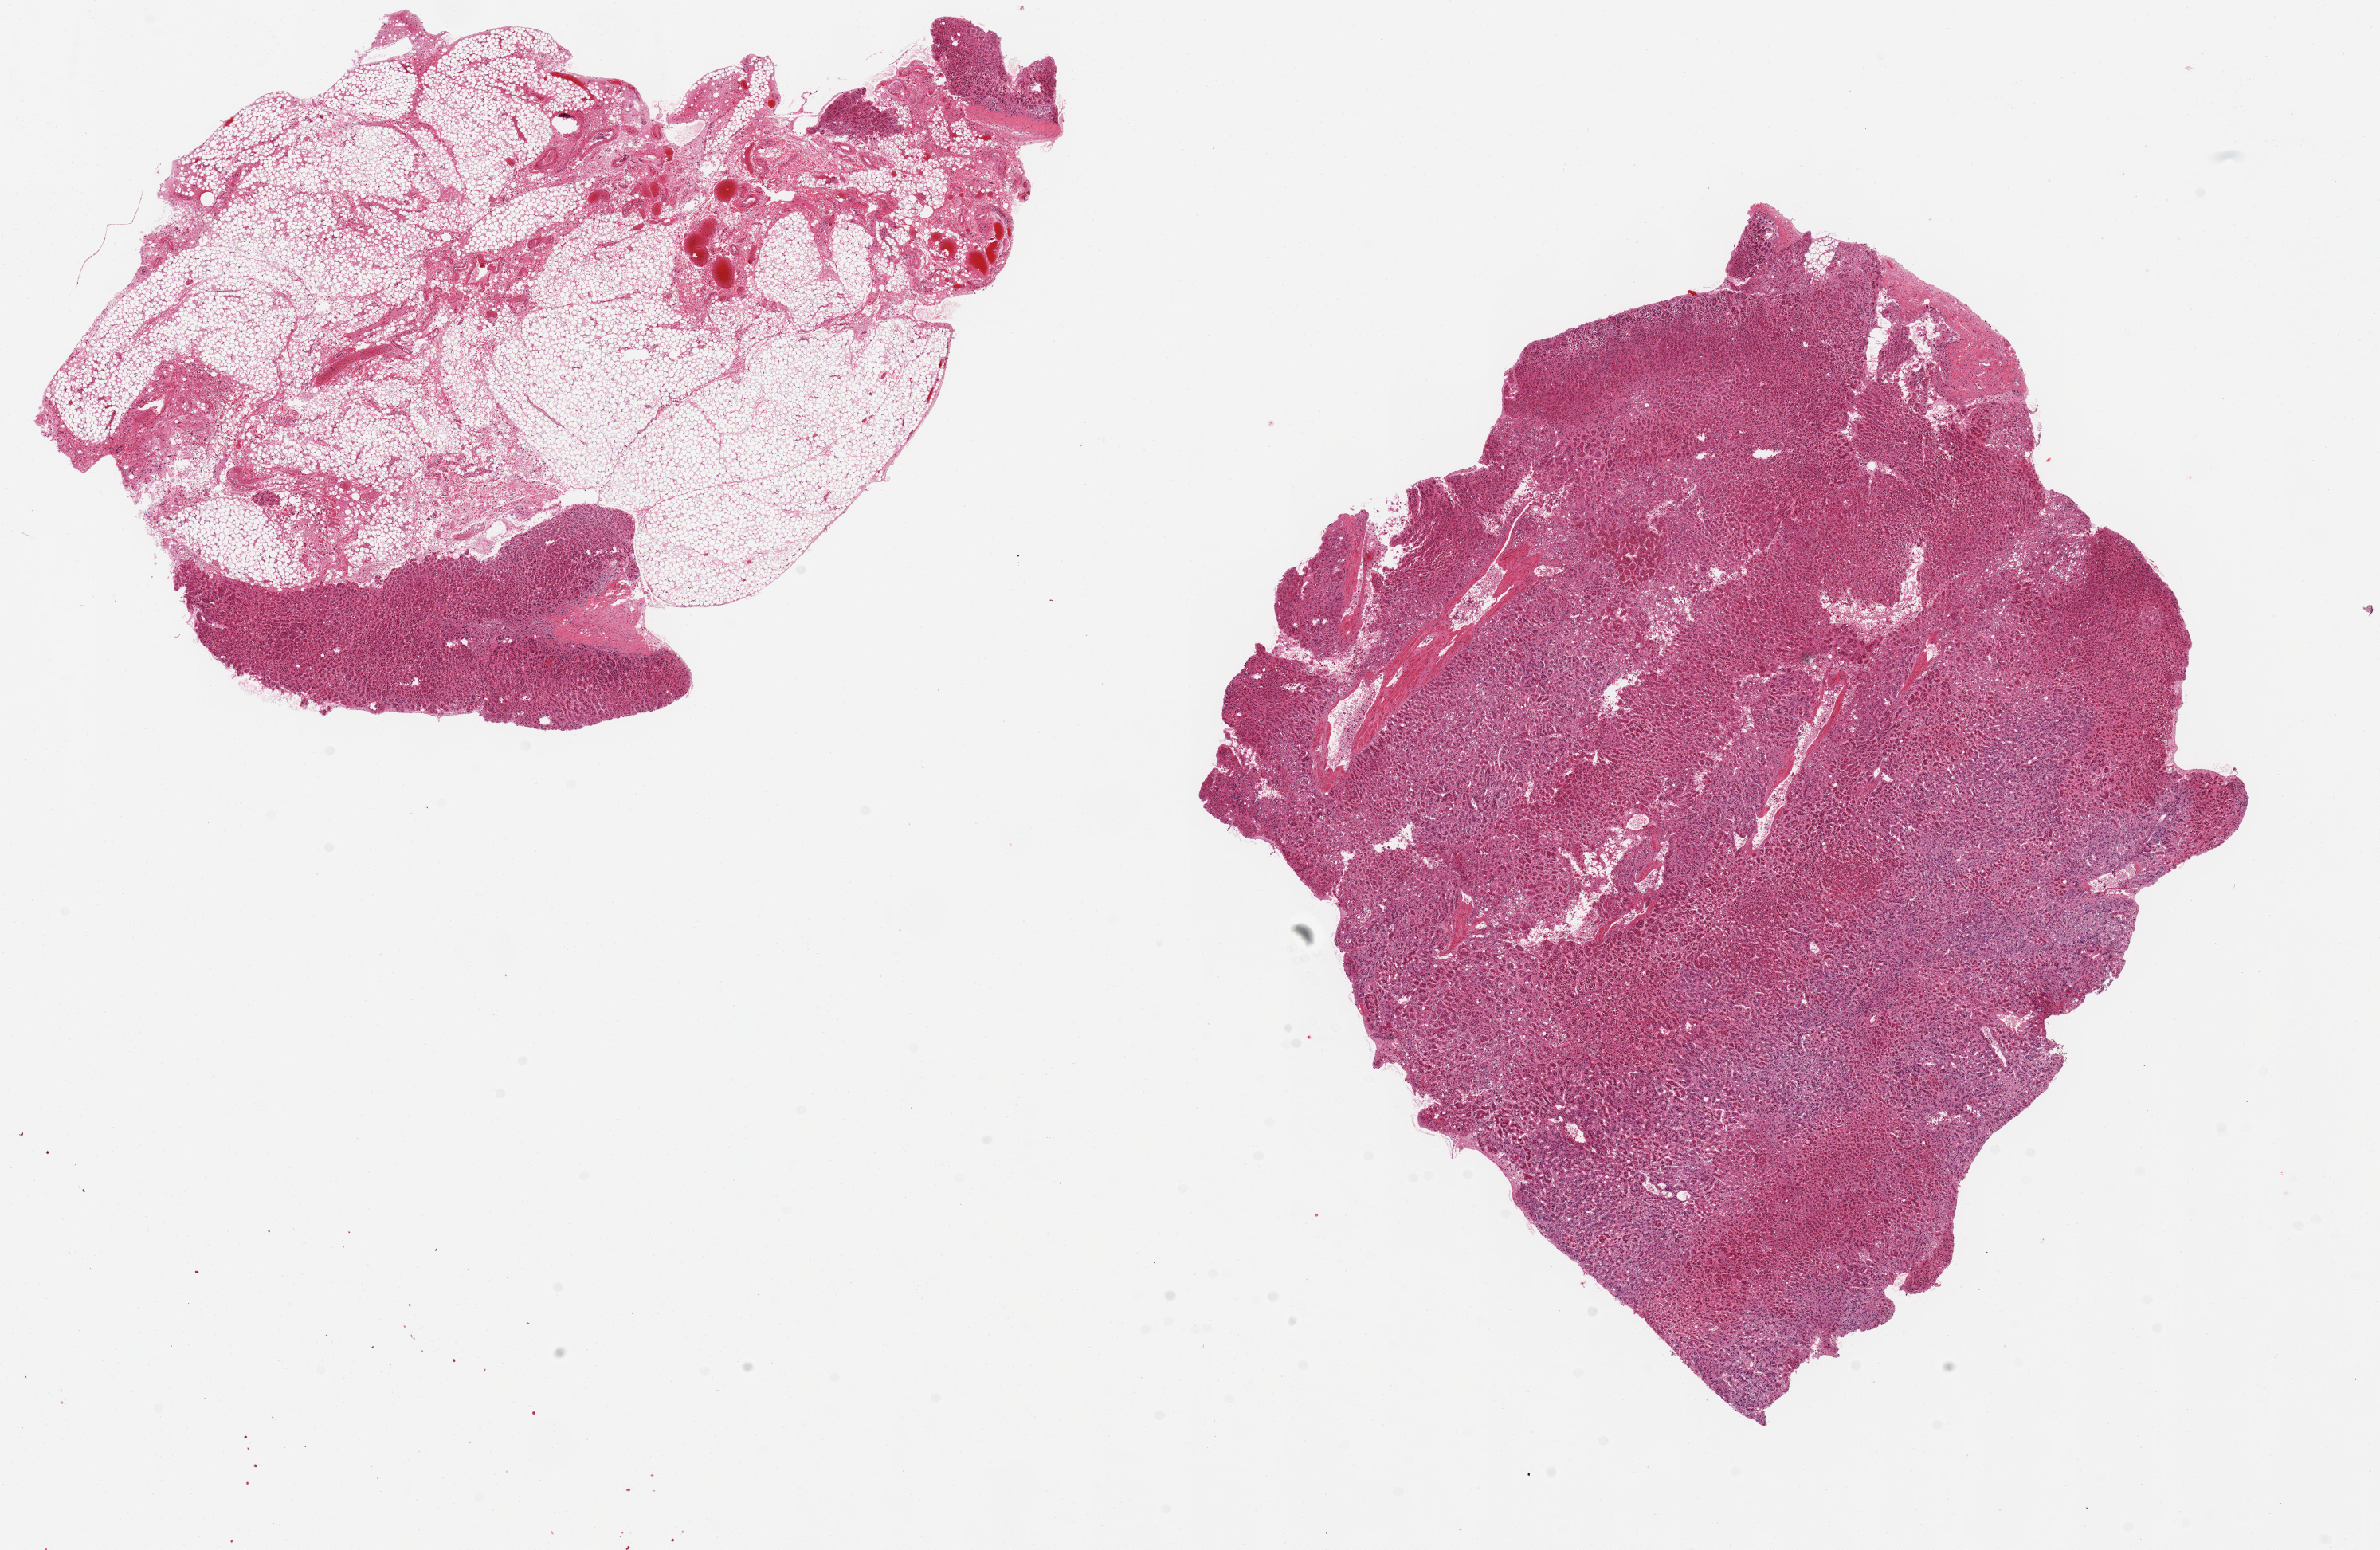
Whole-slide image, hematoxylin and eosin (H&E) stain, a low-resolution overview of the entire scanned area, about 23.6 x 15.4 mm (slide scanned at 20x). PAXgene-fixed, paraffin-embedded tissue. Target tissue: adrenal gland. Donor tissue sample. Donor: female.
Pathologist's review note for this sample: 2 ~9x8mm aliquots; one is ~85% fat; cannot be used; unable to monitor corresponding aliquot.